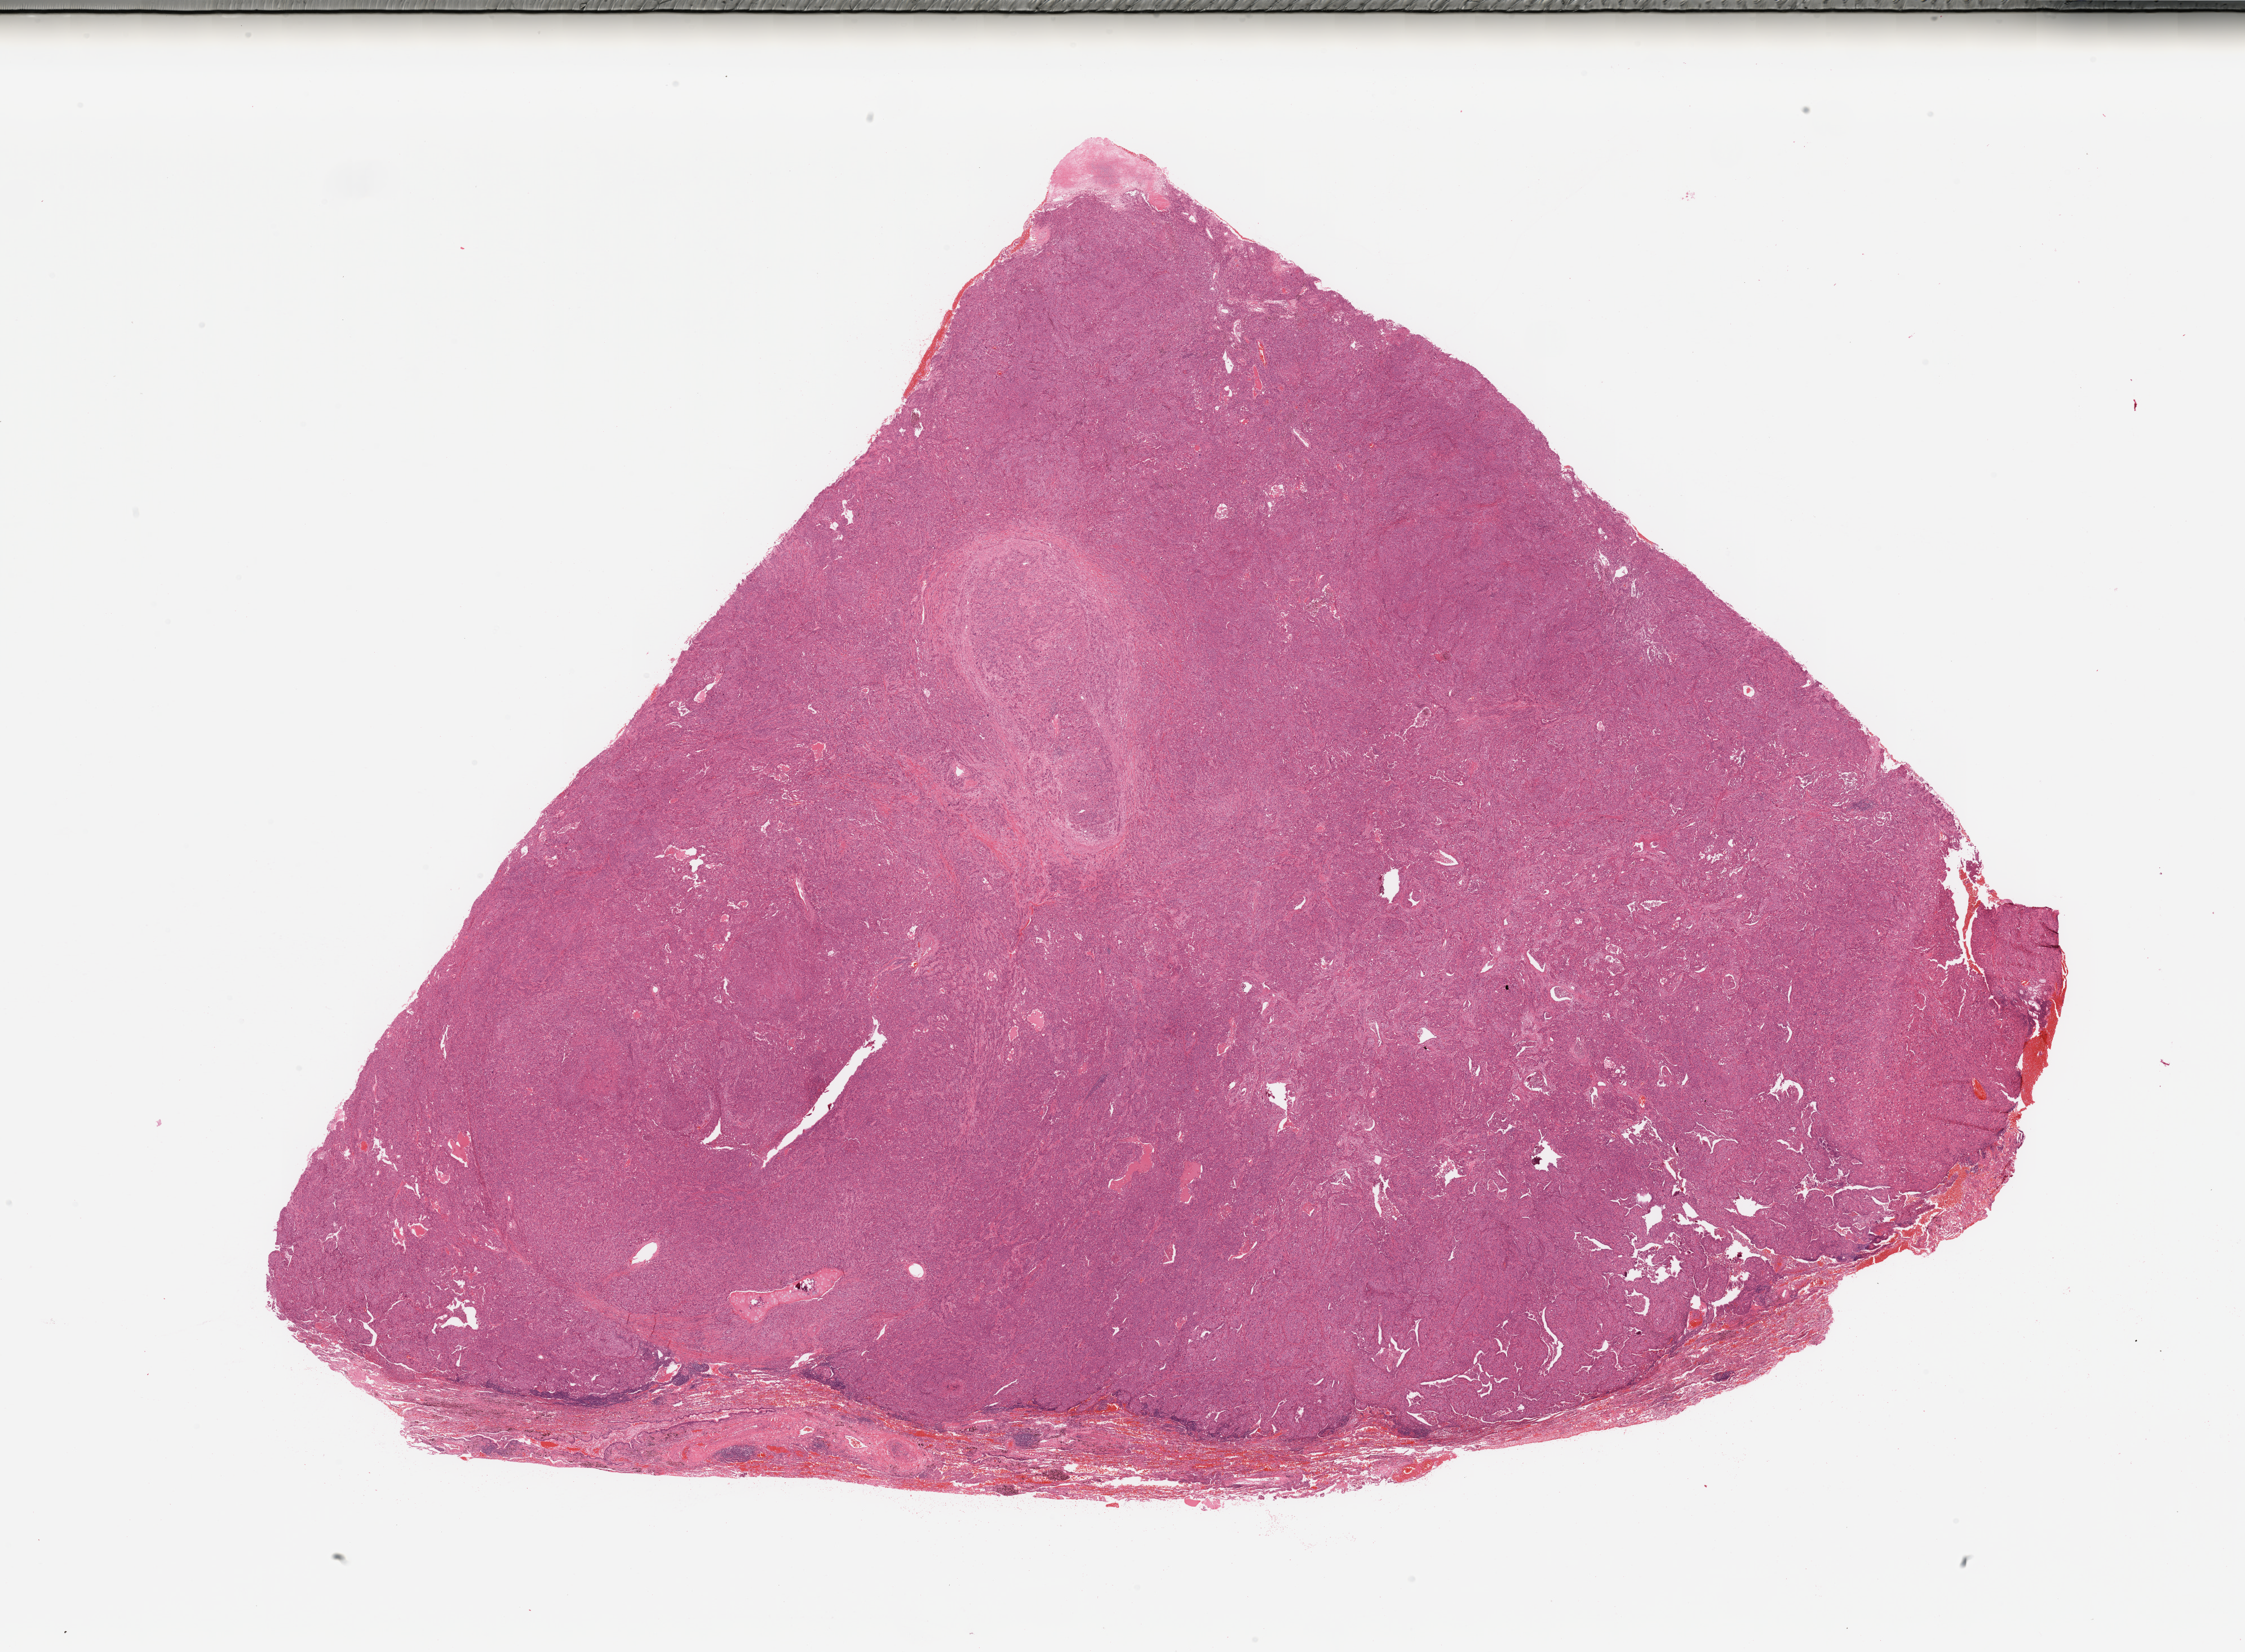
Whole-slide histology image, H&E-stained — low-resolution overview of the scanned area, about 31.5 x 23.2 mm (from a 20x scan). Lung, tissue type not recorded.
Patient diagnosis (cohort enrolment): lung adenocarcinoma (lung).